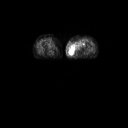
FDG PET of an extremity soft-tissue mass (from a PET/CT study), one axial slice; slice 16 of 91 in the series (ordered by position); 128 × 128 image matrix, field of view 700 × 700 mm. Female patient, age 74 years. From the clinical record (not read from this slice): histological type: pleomorphic leiomyosarcoma; grade: high; site of the primary tumour: left thigh.
Outlined on this slice (expert contour drawn on MRI and transferred to this co-registered scan by the dataset authors):
- gross tumour volume including surrounding oedema: bounding box <69,41,85,54> (left, top, right, bottom; pixels)
- gross tumour volume (mass): <69,47,76,54>